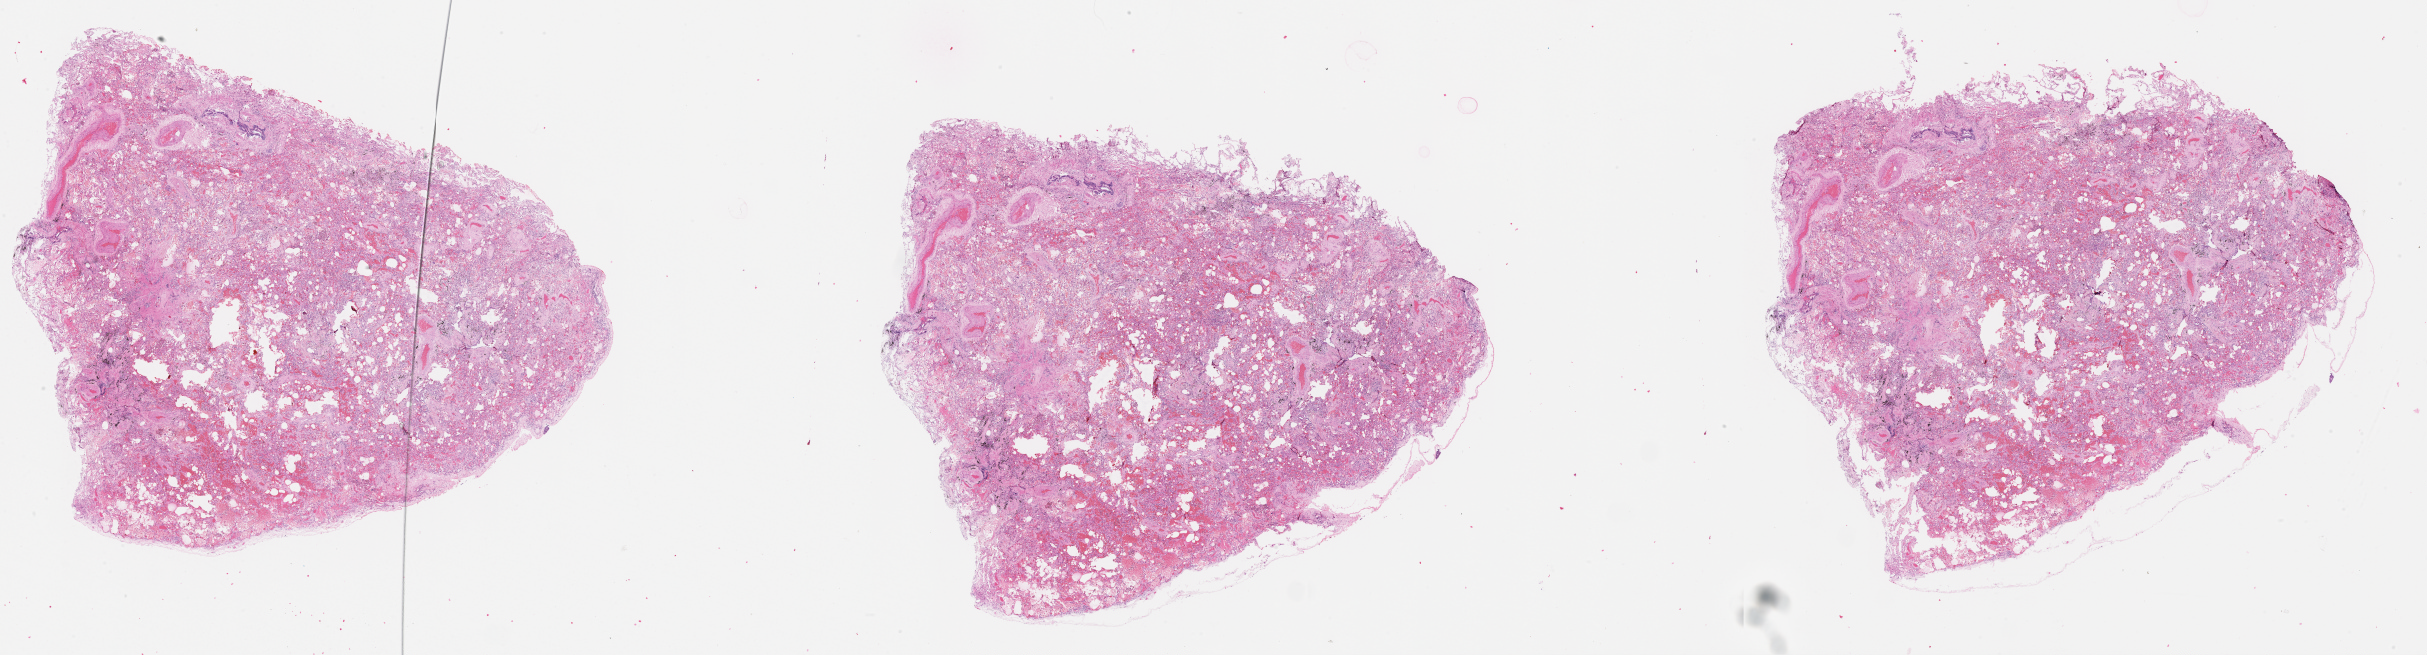
Whole-slide histology image, Hematoxylin and eosin (H&E) stained — shown as a low-resolution overview of the whole scanned area (about 39.1 x 10.5 mm, acquisition: 20x scan); lung, normal (non-tumour) tissue. Patient: male, age 57 years.
* this section: normal (non-tumour) tissue from the same patient
* patient diagnosis (cohort enrolment): squamous cell carcinoma (lung)